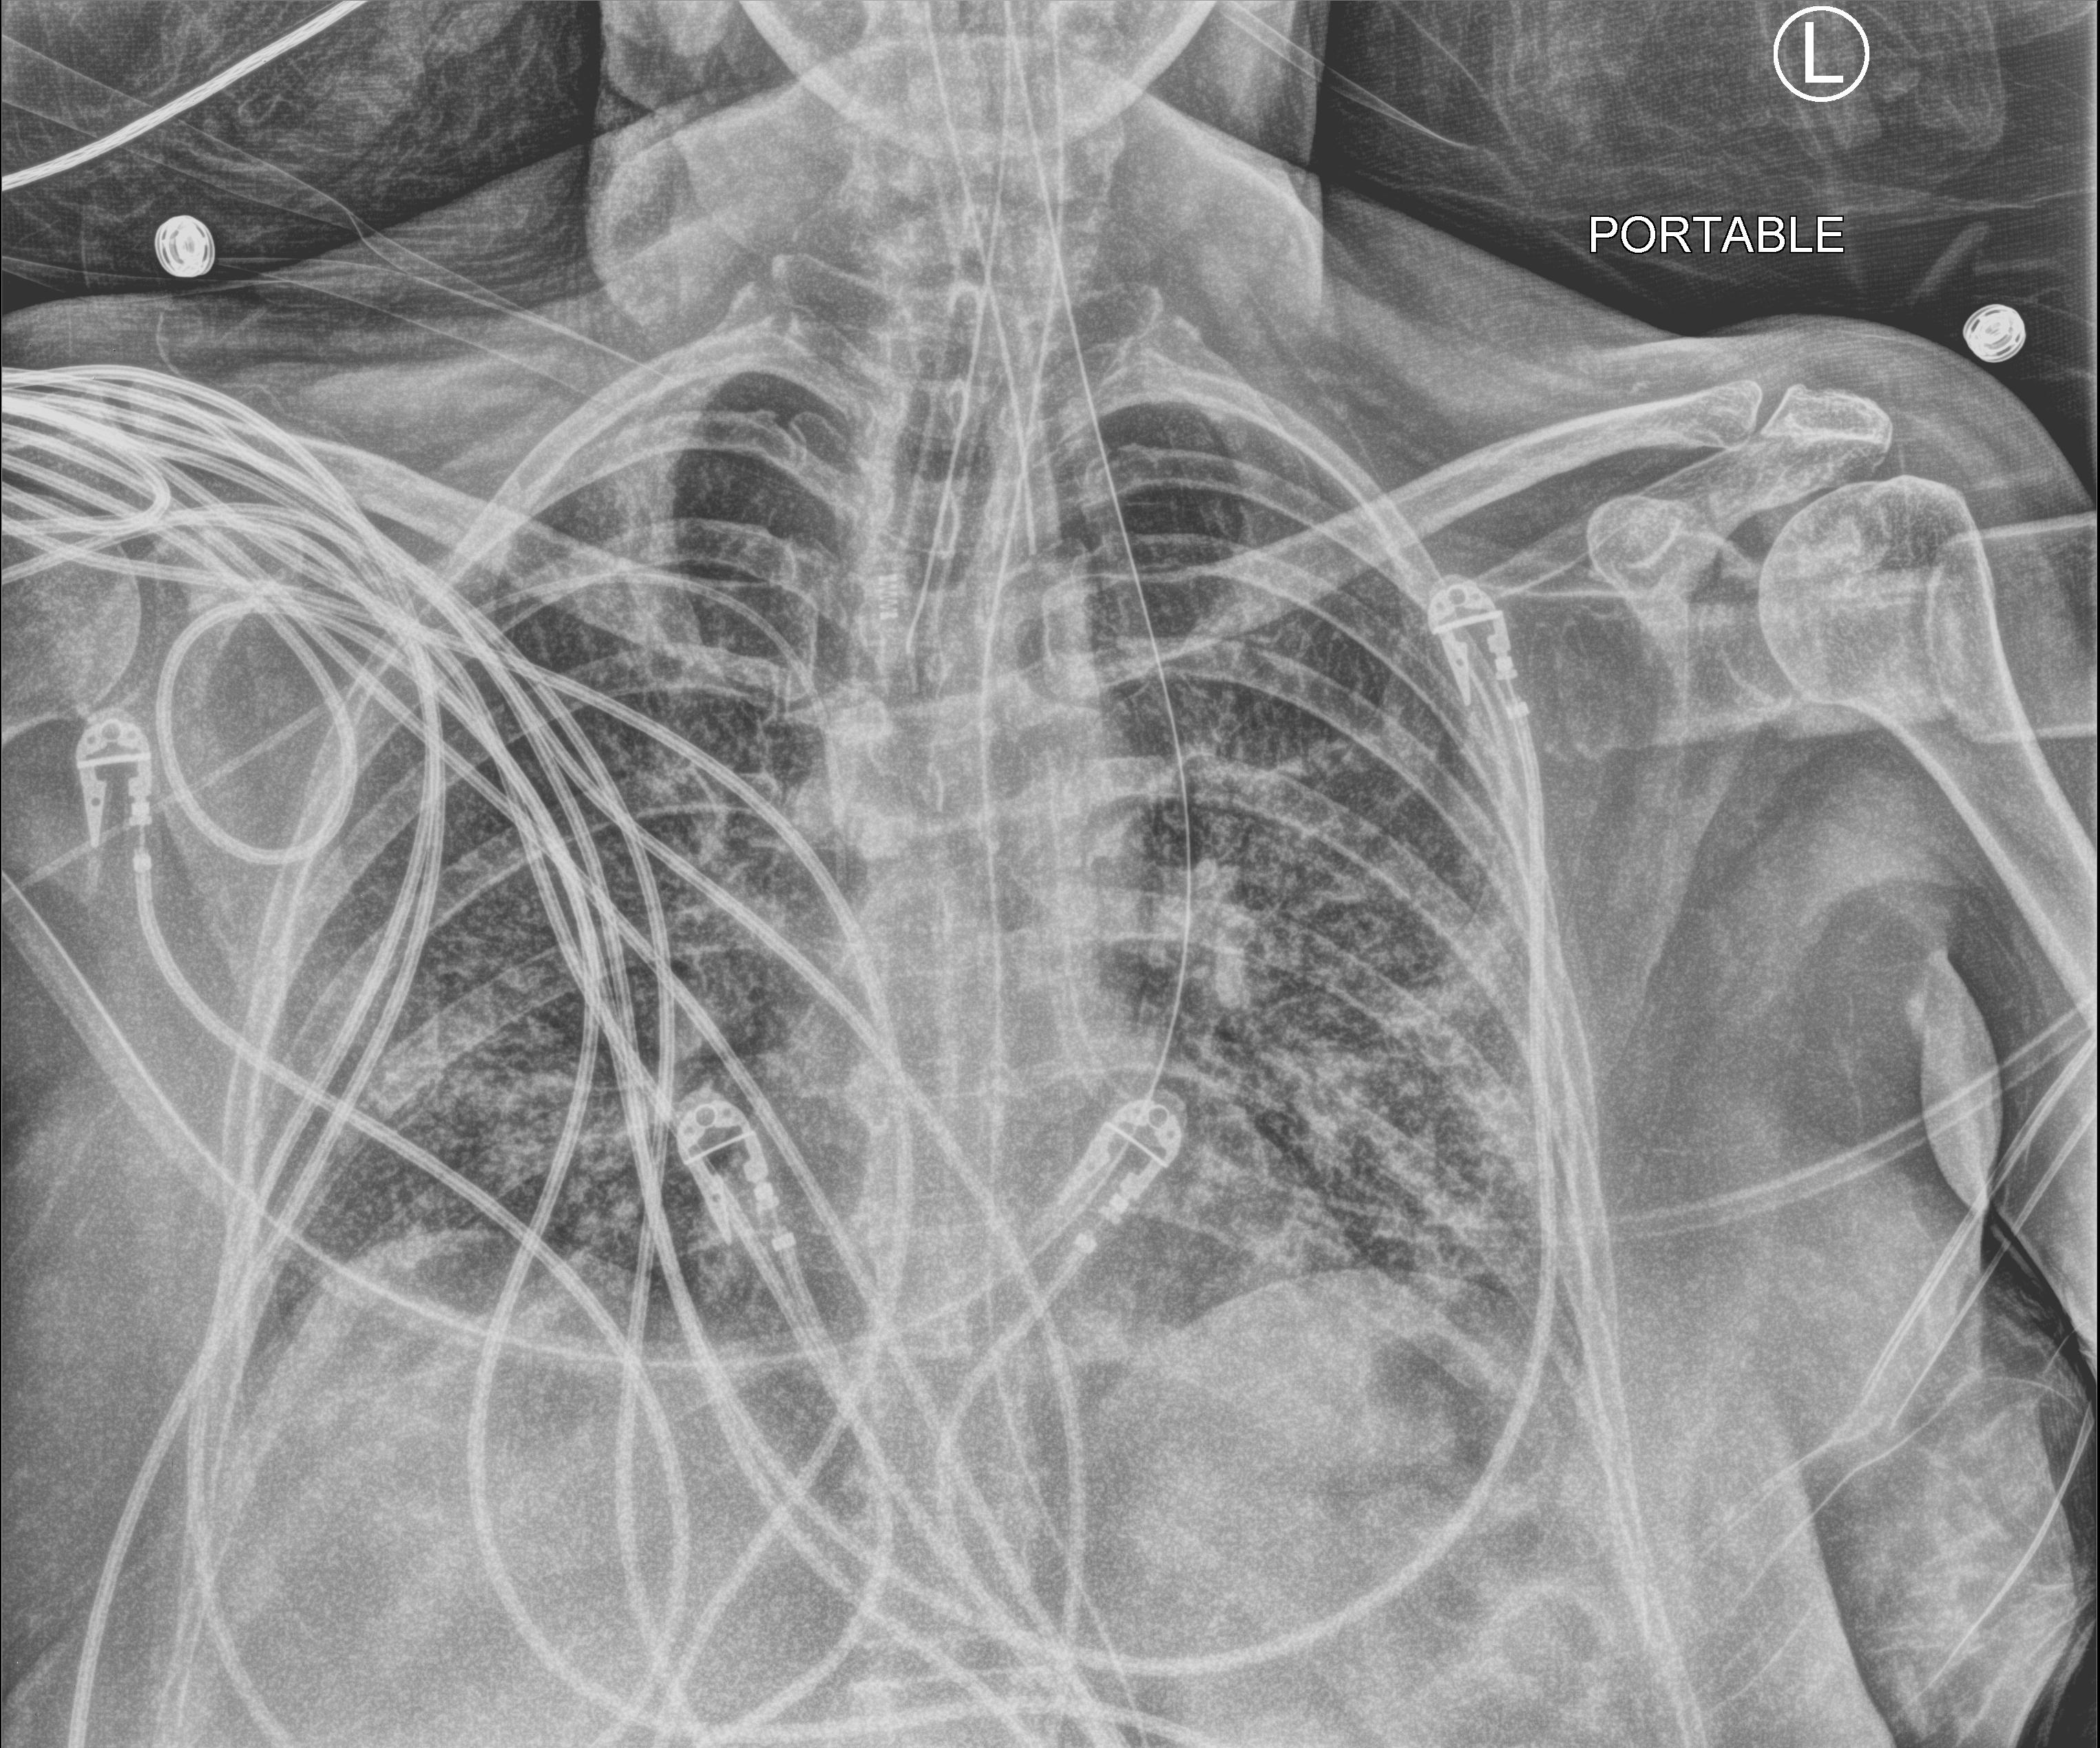
Portable chest radiograph, anteroposterior (AP) projection. Patient hospitalised with COVID-19; female, aged 60–74 years.
Admission-level facts for this patient (not findings on this image; timing relative to this image not recorded): mechanically ventilated during this hospital stay: yes; length of hospital stay: 43 days; admitted to intensive care during this hospital stay: yes.